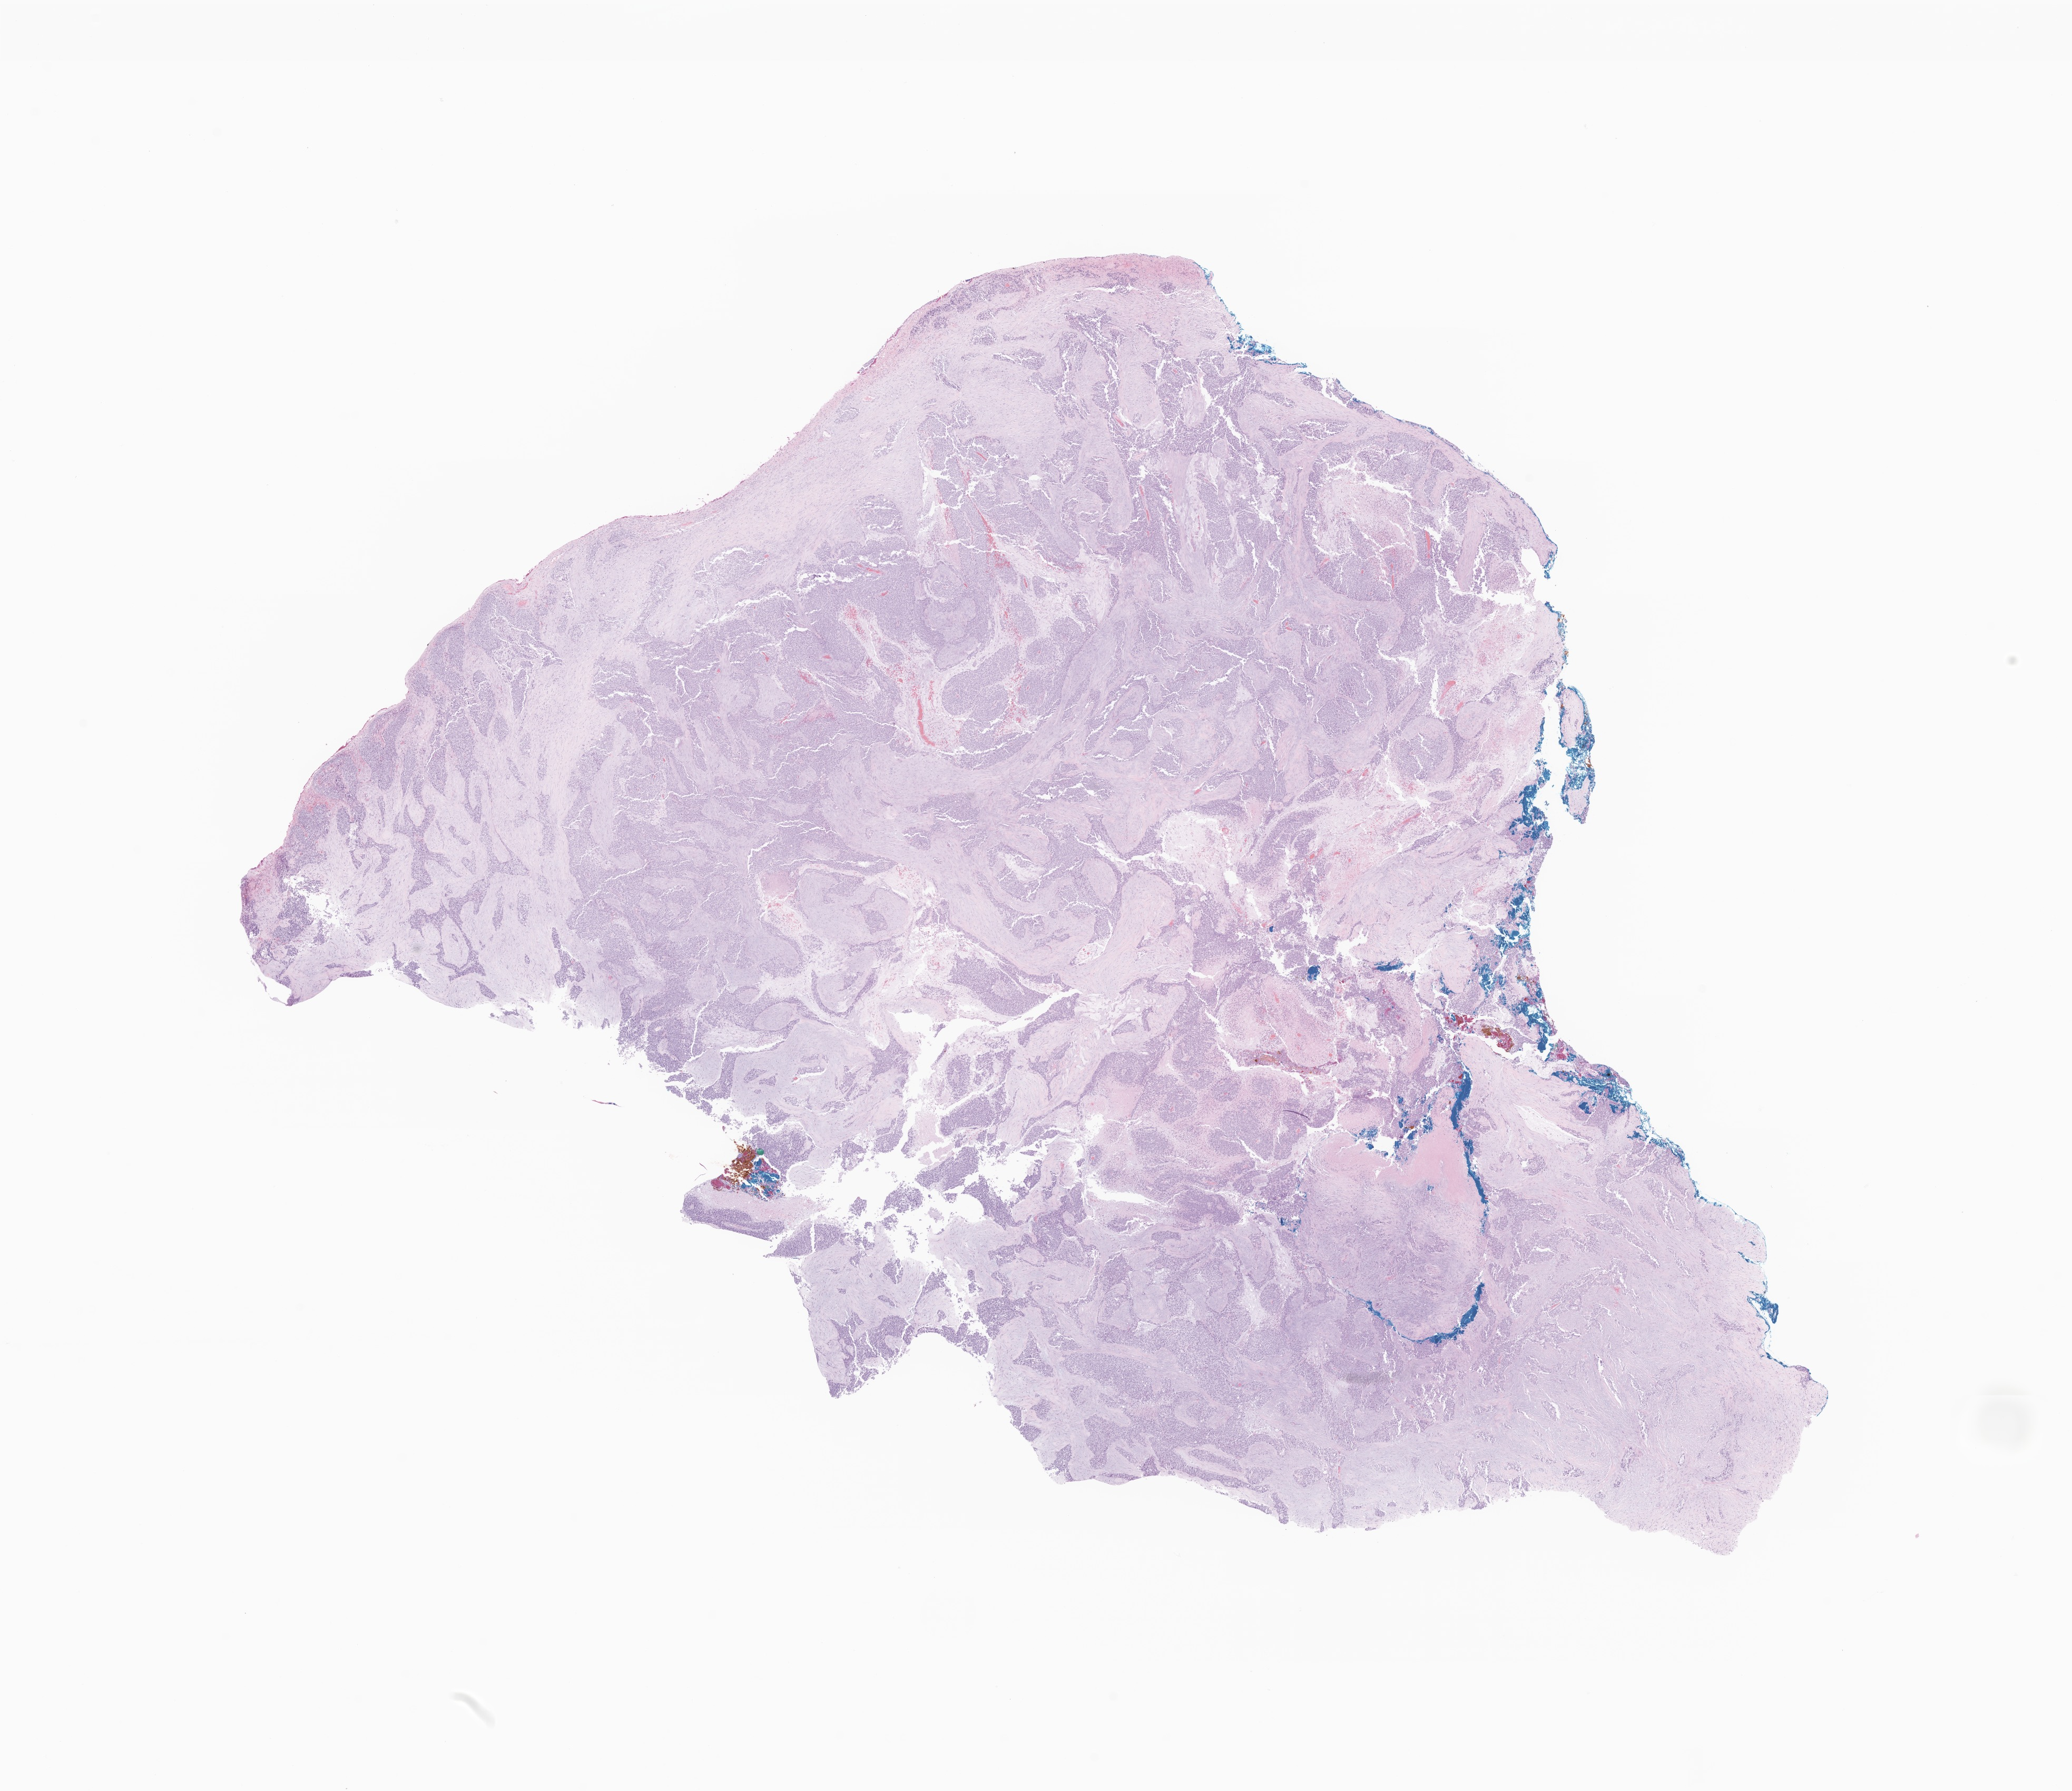
Hematoxylin and eosin (H&E) whole-slide image of tumor tissue from the ovary, shown as a low-resolution overview of the whole scanned area (about 16.6 x 14.3 mm). Formalin-fixed paraffin-embedded section. Female patient, age 201 months (16 years 9 months).
* recorded diagnosis: Desmoplastic small round cell tumor